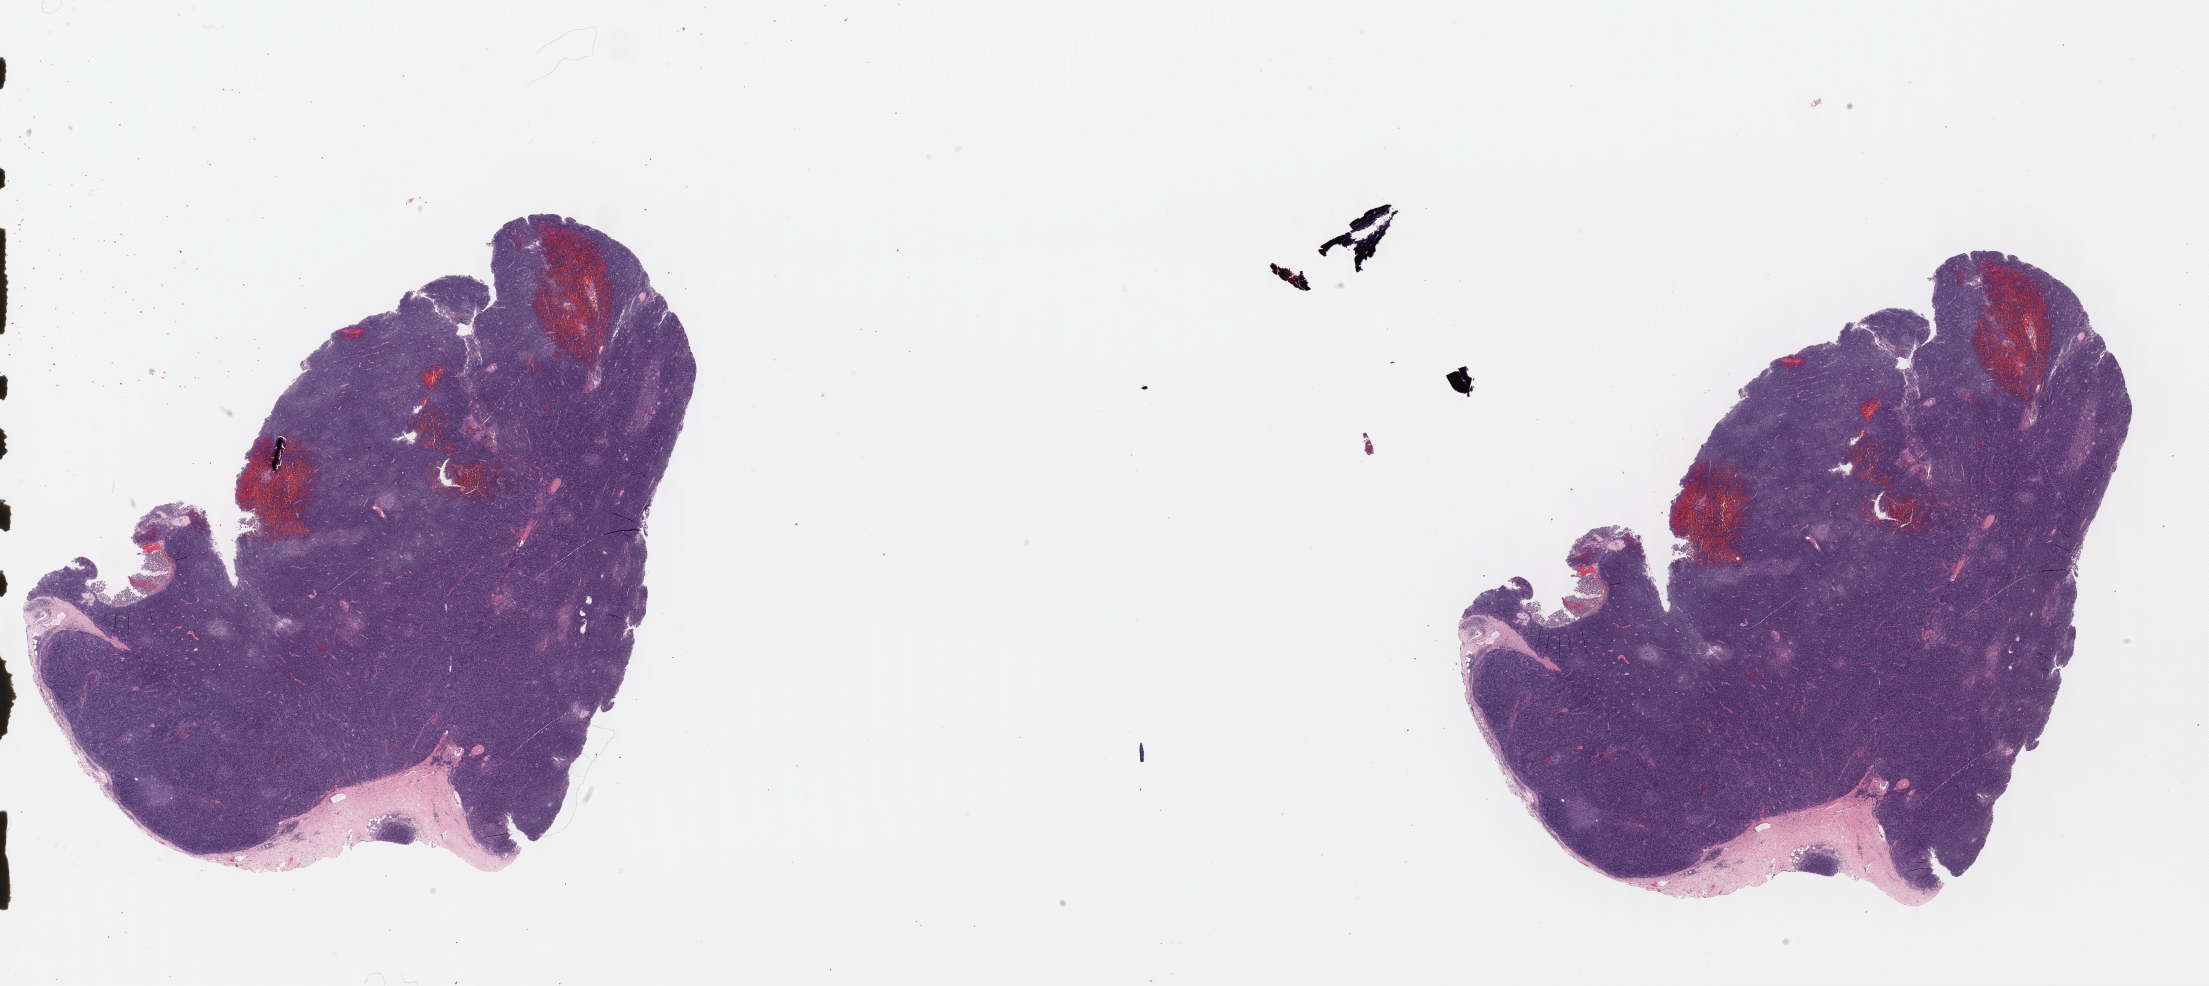
Digitized H&E-stained tissue section (whole slide) — a low-resolution overview of the entire scanned area, about 35.7 x 16.0 mm (slide scanned at 40x); FFPE section; sample: primary tumour, thymus. Patient: female, age at initial diagnosis 46 years.
- diagnosis: Thymoma, type B1, malignant